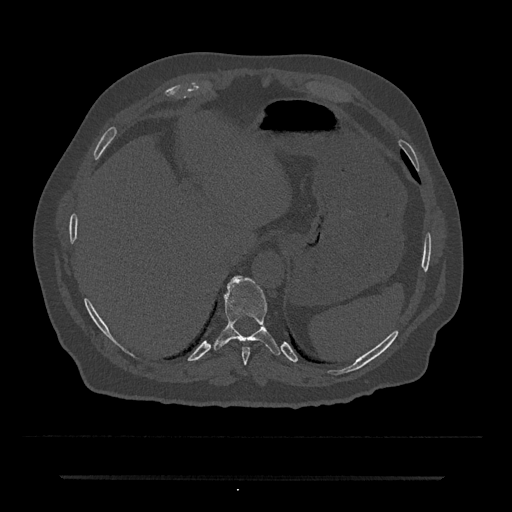
CT including the spine, one axial slice. Position 238 of 797 along the scan axis. Reconstruction kernel Br40s/3. 120 kVp. Bone window (W 1800 / L 400 HU). 0.5 mm slice thickness. 512 × 512 image matrix, field of view 437 × 437 mm. Male patient, age 69 years. From the clinical record (not read from this slice): primary cancer: prostate.
Annotated regions visible in this slice (semi-automatic segmentation, software-assisted and operator-edited):
- T10 vertebra: bounding box <213,276,281,355> (left, top, right, bottom; pixels)
- T9 vertebra: <242,347,250,365>